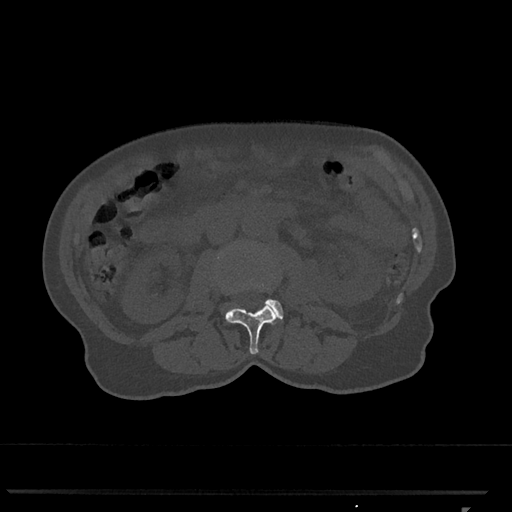
CT including the spine, one axial slice; position 311 of 793 along the scan axis; reconstruction kernel Br40s/3; bone window (W 1800 / L 400 HU); 0.5 mm slice thickness; 512 × 512 image matrix. Female patient, age 62 years. Case-level facts recorded for this patient, not image findings: primary cancer: renal.
Annotated regions visible in this slice (semi-automatically segmented with operator editing):
- L2 vertebra: bounding box <218,257,278,354> (left, top, right, bottom; pixels)
- L3 vertebra: <227,285,283,320>